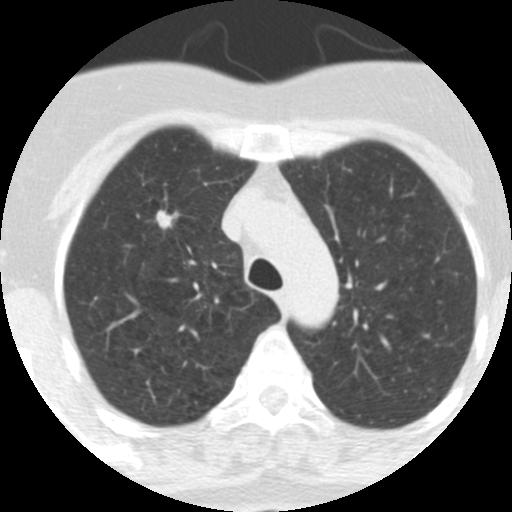
Low-dose screening chest CT, one axial slice; slice 241 of 313 in the series (ordered by position); lung window (W 1500 / L -600 HU); 2.5 mm slice thickness; 512 × 512 image matrix.
Structures marked on this image (expert manual segmentation):
- lesion 1 (tumor, upper lobe of right lung): bounding box [x1, y1, x2, y2] px = [156, 210, 179, 229]